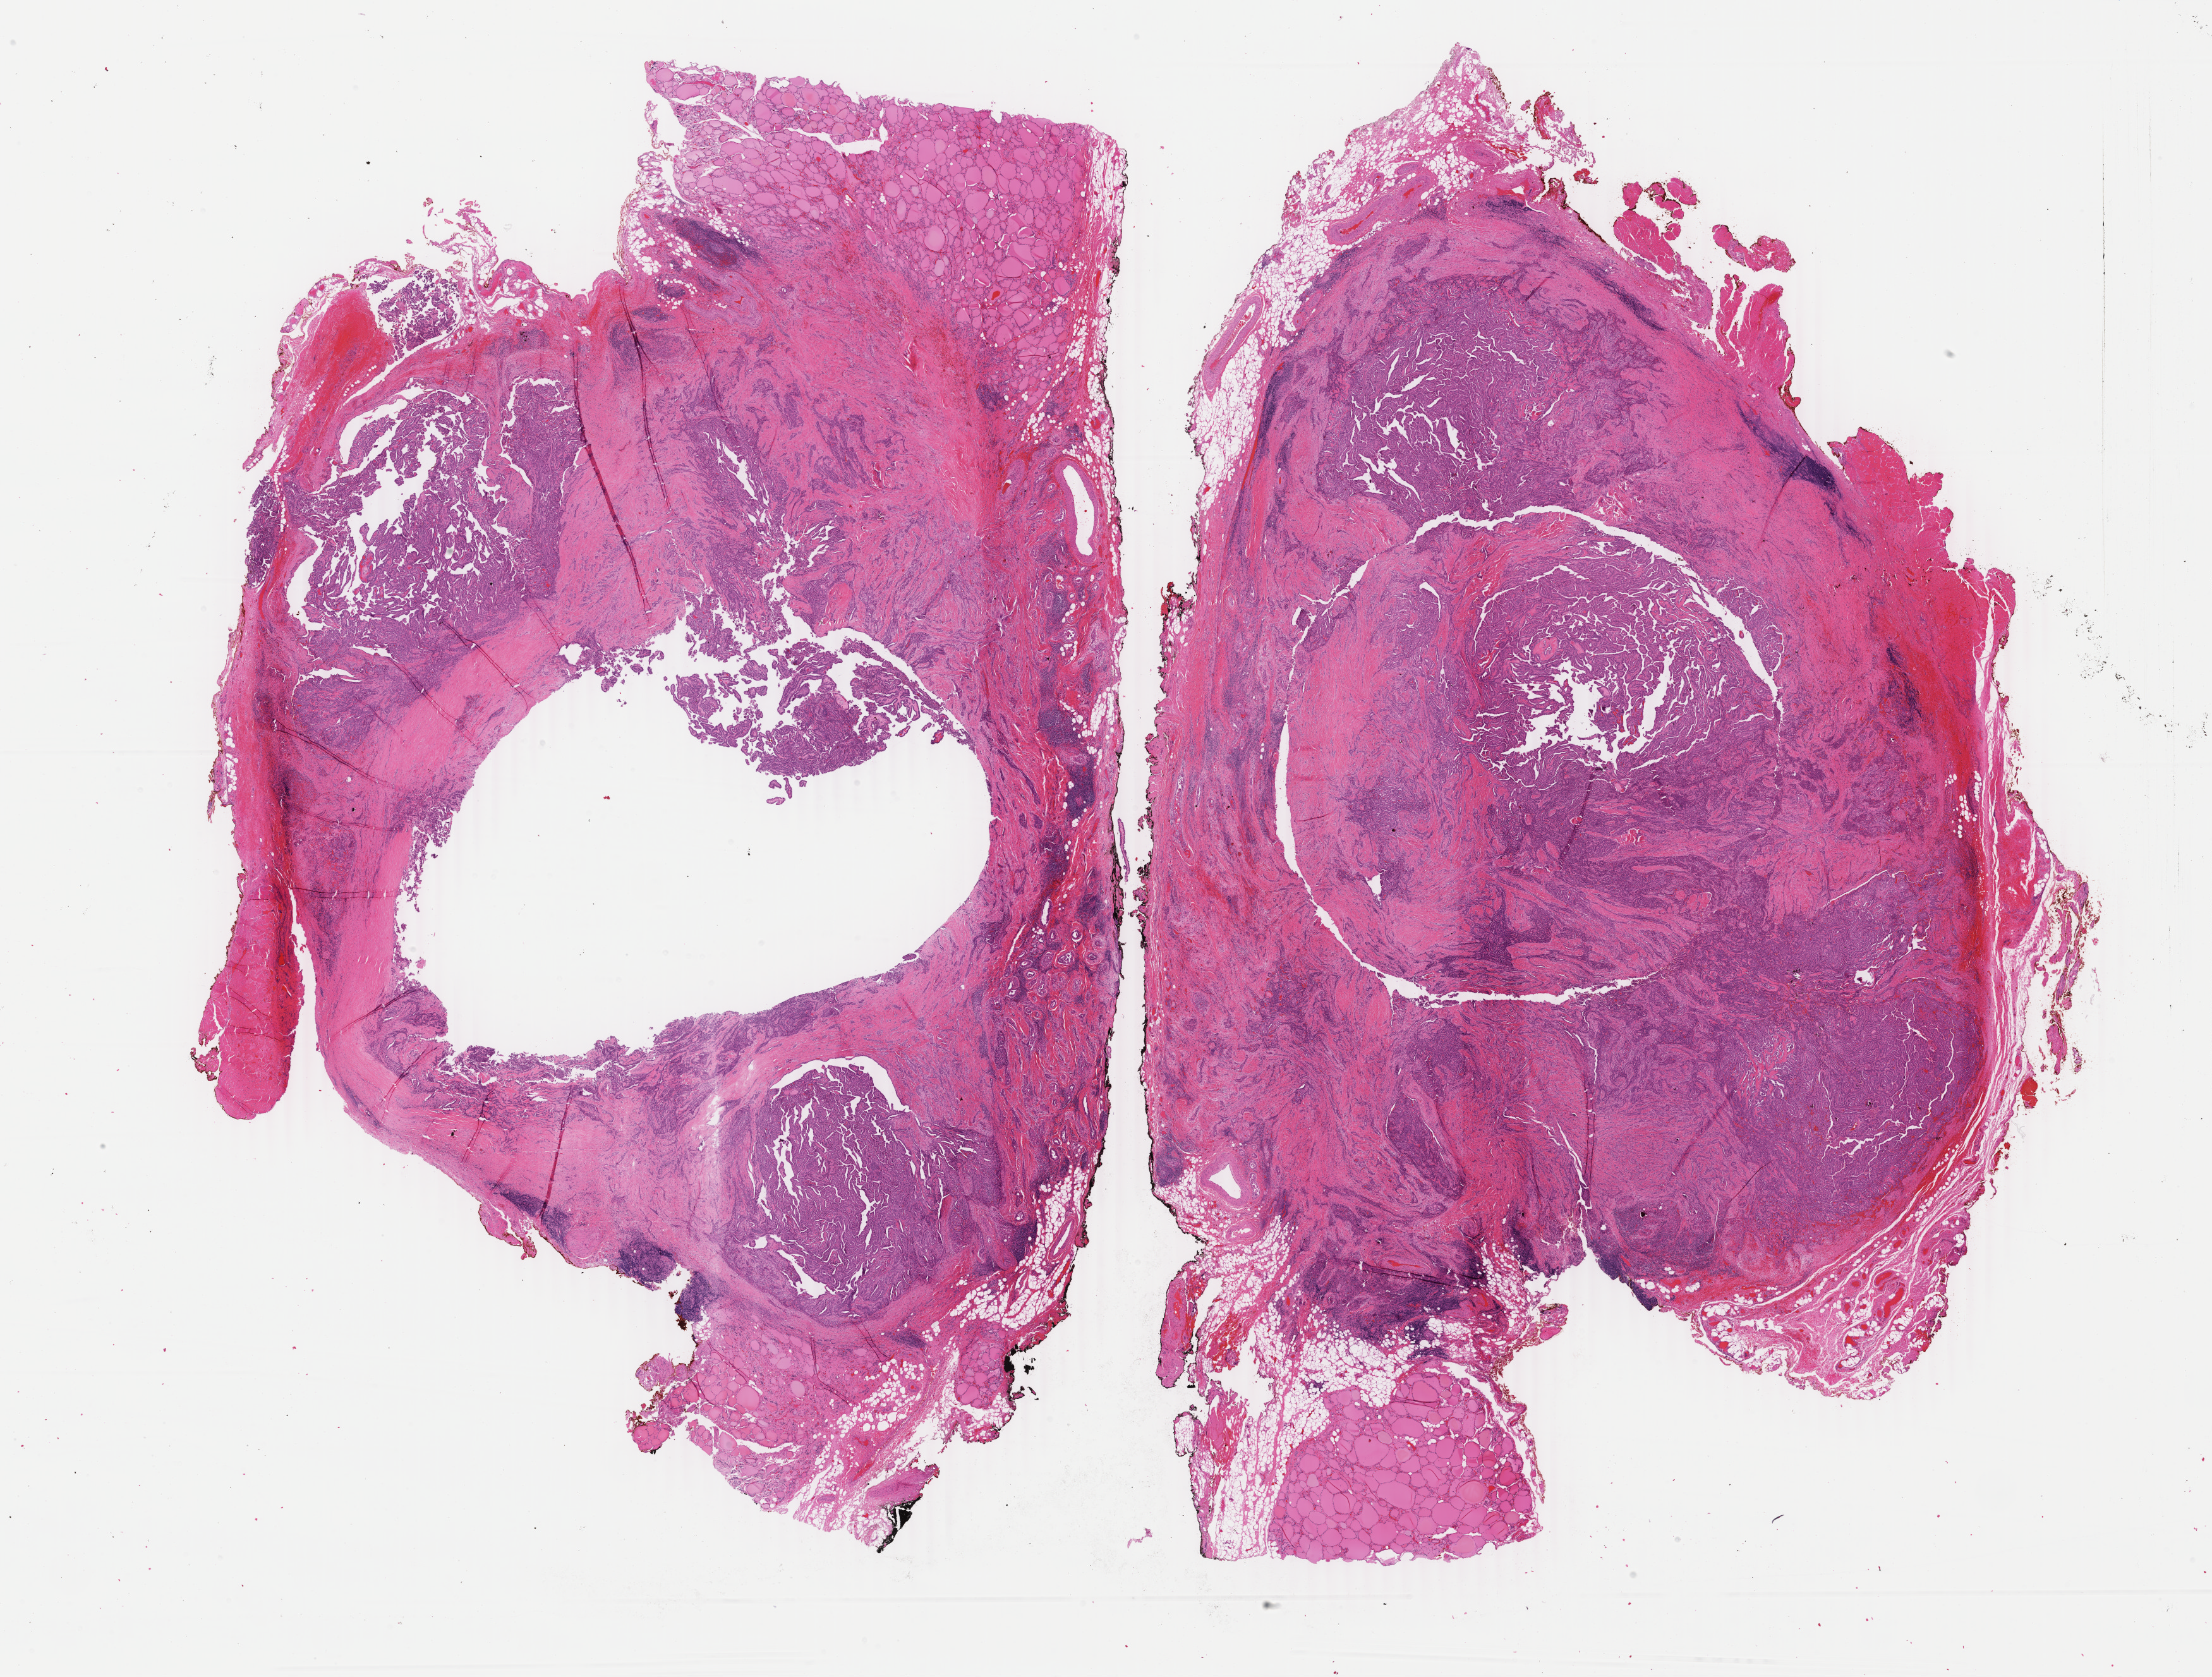
Whole-slide histology image, H&E, shown as a low-resolution overview of the whole scanned area (about 27.8 x 21.1 mm, slide scanned at 40x). Formalin-fixed paraffin-embedded (FFPE) diagnostic section. Thyroid, primary tumour sample. Female patient; age at initial diagnosis 51 years.
• histologic diagnosis: Papillary carcinoma, columnar cell (thyroid gland)
• laterality: midline
• TNM: T3 NX MX
• AJCC pathologic stage: III (7th edition)